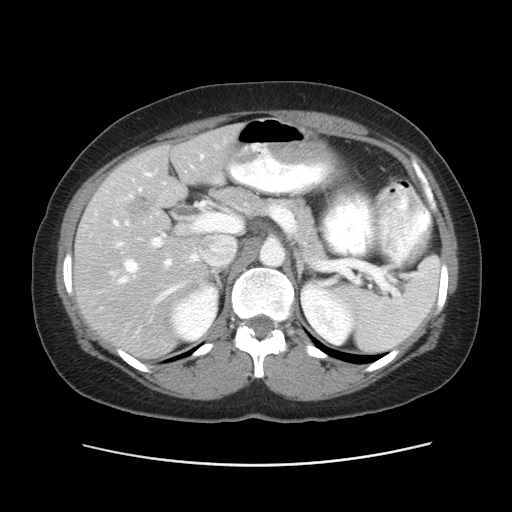
Contrast-enhanced abdominal CT, one axial slice; position 32 of 52 along the scan axis; reconstruction kernel STANDARD; 120 kVp; intravenous contrast given; soft-tissue window (W 400 / L 40 HU); 512 × 512 image matrix, field of view 362 × 362 mm. Female patient, age 48 years. From the clinical record (not read from this slice): diagnosis: colorectal cancer liver metastases, imaged before liver resection; multiple liver metastases: yes; largest metastasis: 4.5 cm; disease in both lobes: yes.
Structures marked on this image (manually delineated by an expert):
- hepatic veins: bounding box <119,146,218,300> (left, top, right, bottom; pixels)
- liver: <75,126,238,356>
- planned liver remnant (the part of the liver to remain after resection): <163,126,239,195>
- portal vein (with intrahepatic branches): <110,155,210,282>
- liver metastasis: <126,194,154,221>